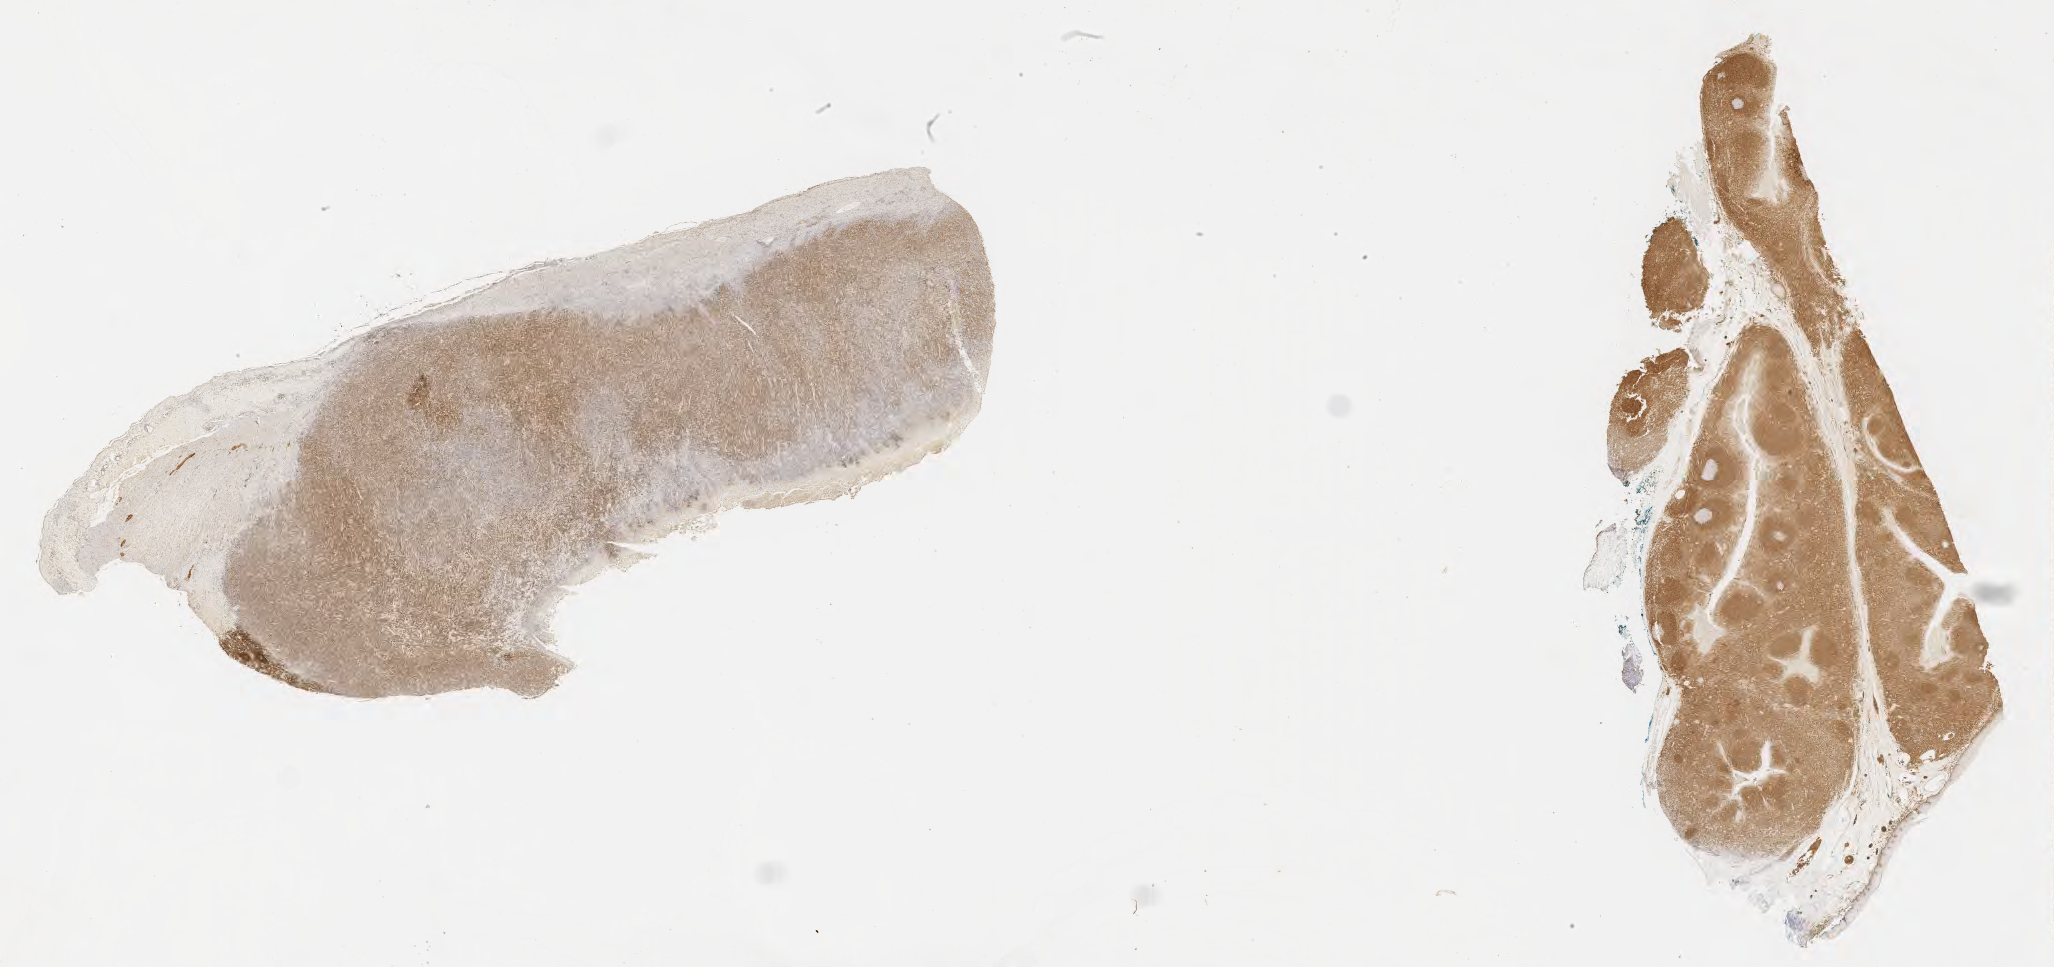
Whole-slide image, immunohistochemical stain for BCL2, low-resolution overview of the scanned area, about 33.2 x 15.6 mm, tumor tissue, site: small intestine. Patient: male, age at initial diagnosis 3 years.
Histologic diagnosis: Burkitt lymphoma, NOS.